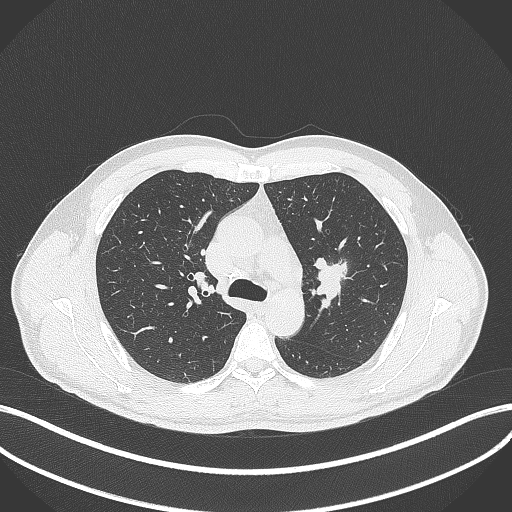
Chest CT, one axial slice. Slice 284 of 392 in the series (ordered by position). 120 kVp. Lung window (W 1500 / L -600 HU). 1 mm slice thickness. 512 × 512 image matrix. Male patient, age 50 years. Case-level facts recorded for this patient, not image findings: clinical TNM (as recorded): T1c N1 M1b.
Structures marked on this image (rectangle marked by the reading radiologist):
- lung tumour (recorded histology: squamous cell carcinoma): bounding box (x1, y1, x2, y2) in pixels: (309, 253, 349, 301)